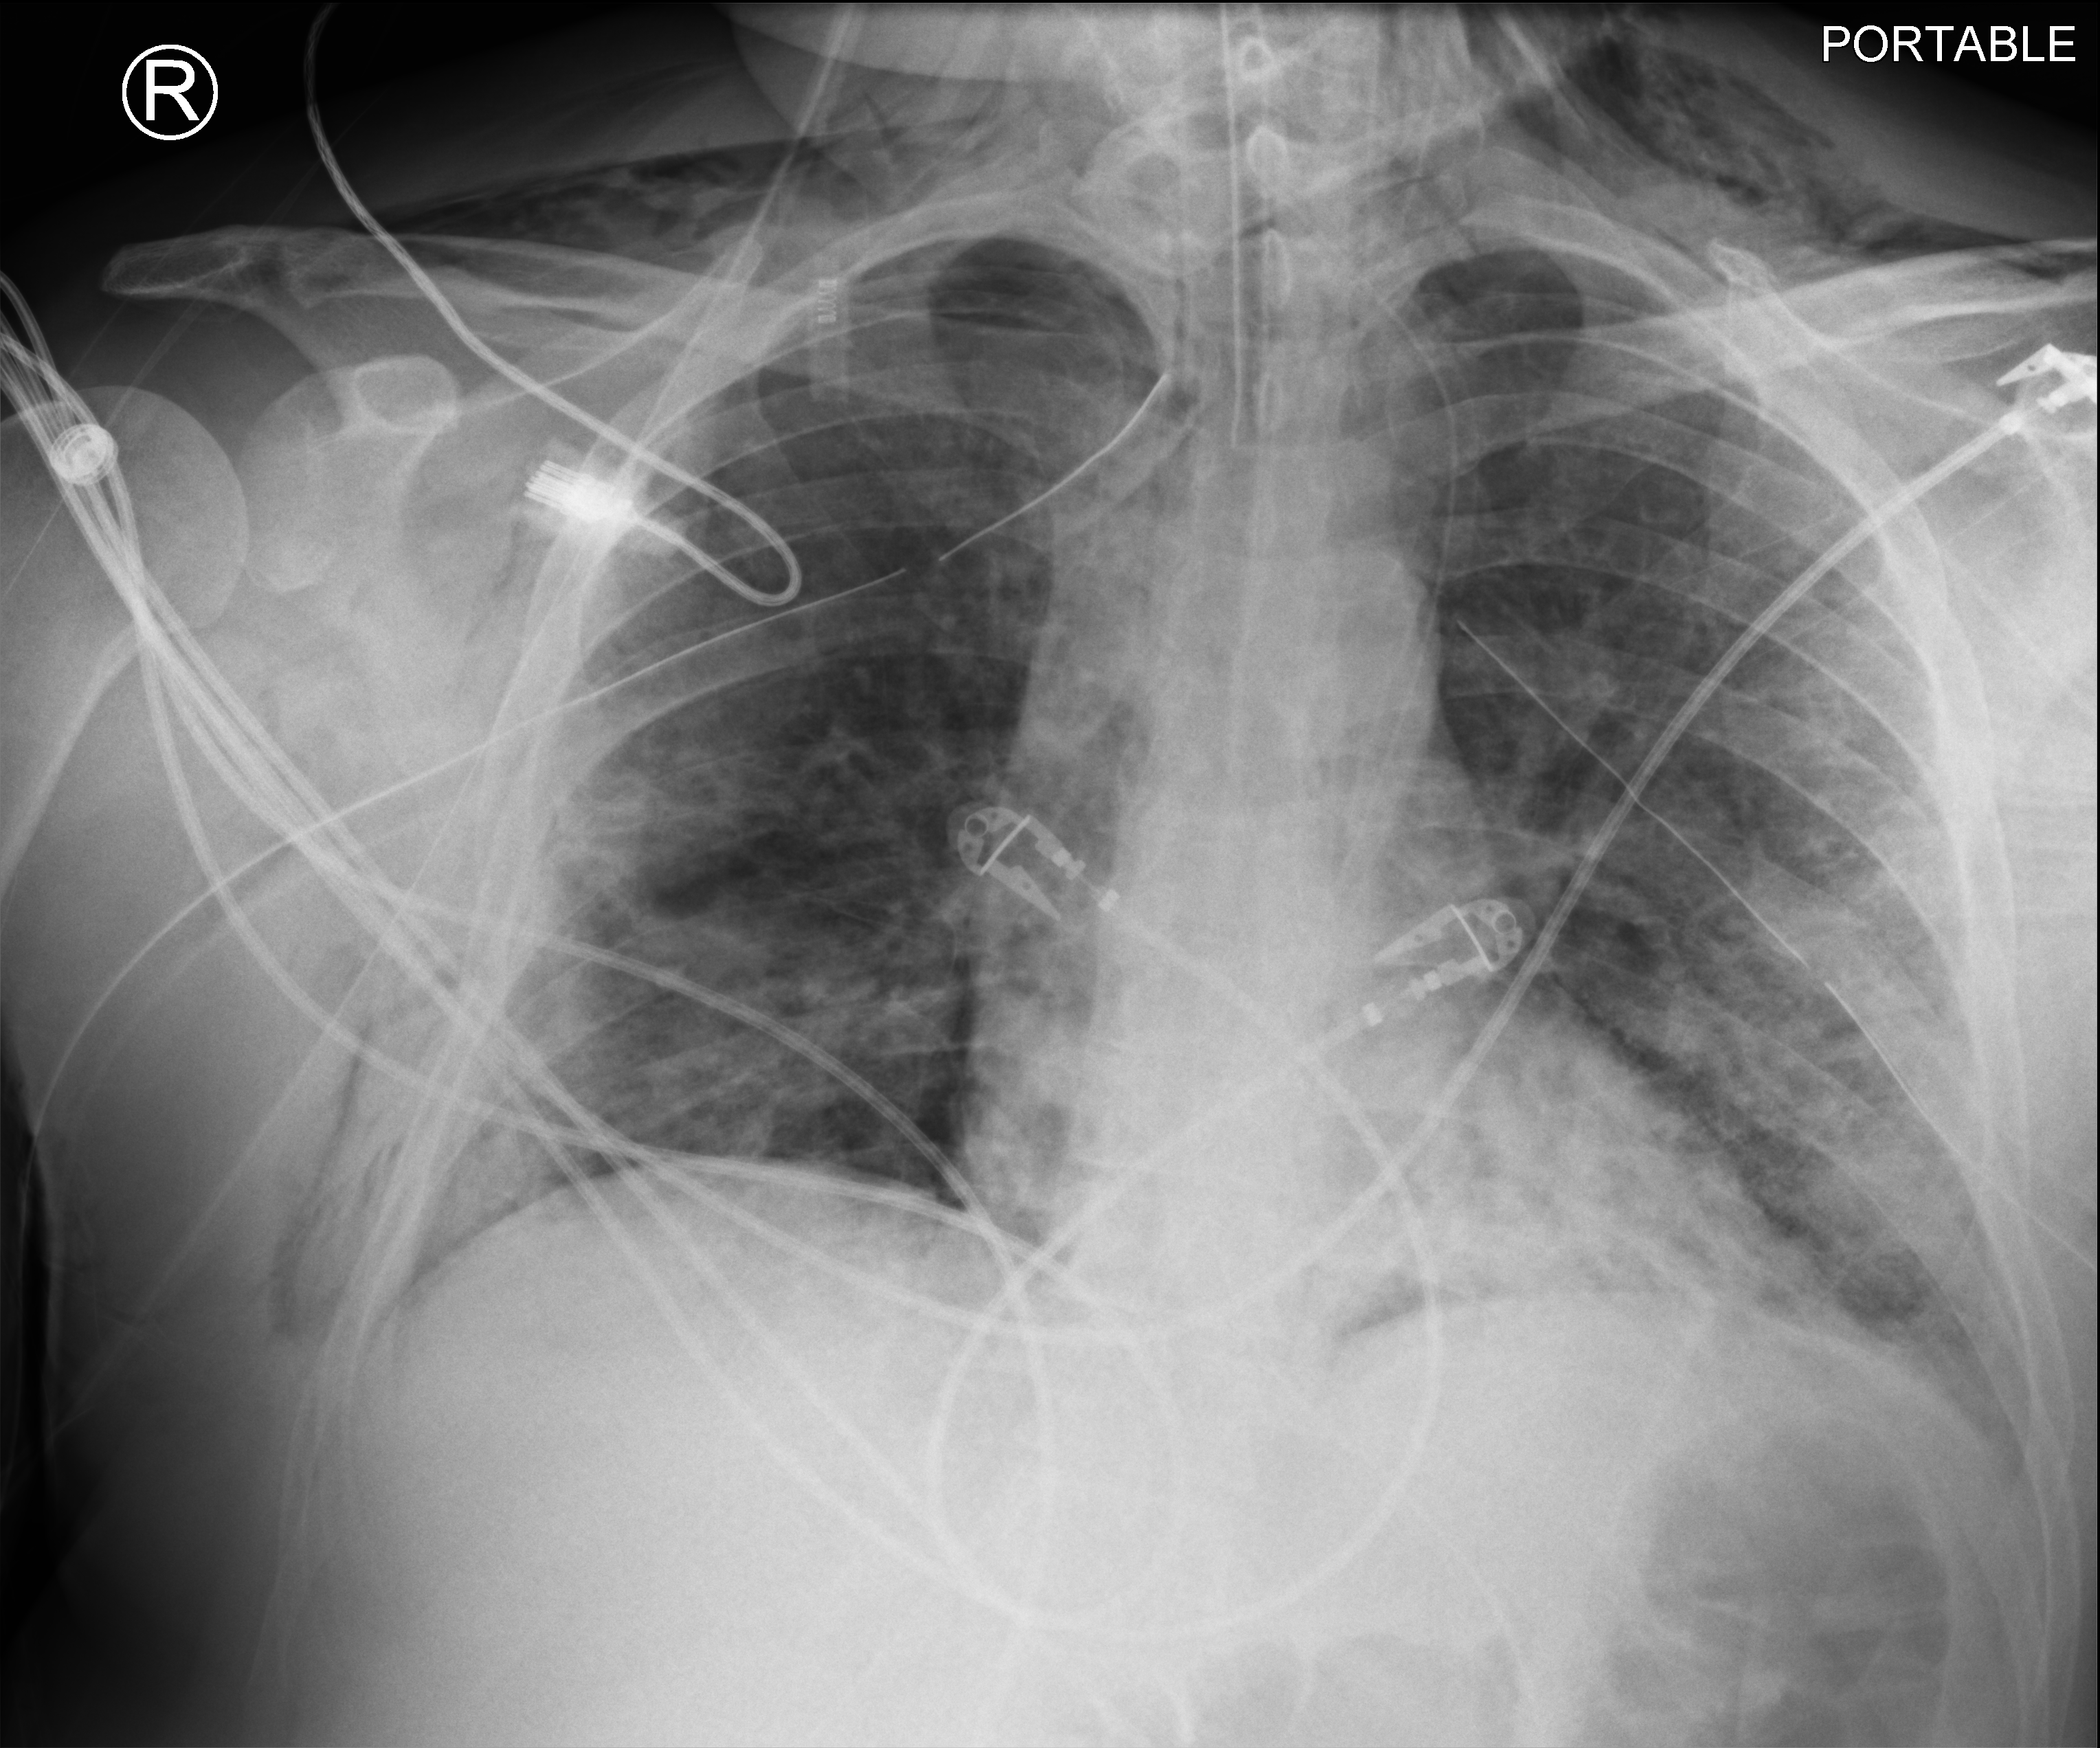
Chest X-ray (portable), anteroposterior (AP) projection. Male patient hospitalised with COVID-19, age 18–59 years.
From the hospital-stay record, not from the radiograph (when in the stay this image was taken is not recorded): mechanically ventilated during this hospital stay: yes; length of hospital stay: 63 days.